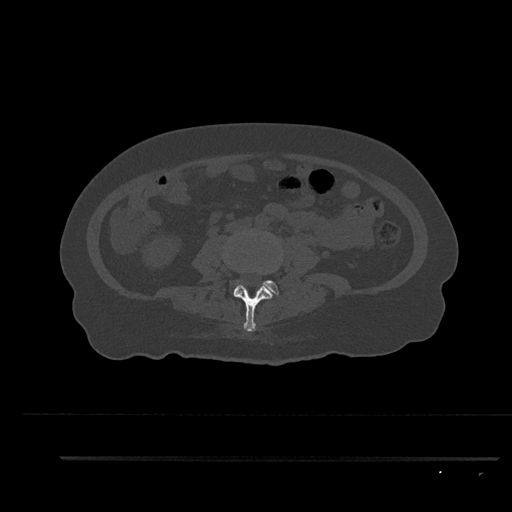
CT including the spine, one axial slice; slice 61 of 797 in the series (ordered by position); reconstruction kernel Br40s/3; 120 kVp; bone window (W 1800 / L 400 HU); 0.5 mm slice thickness; 512 × 512 image matrix, field of view 408 × 408 mm. Female patient, age 44 years. Case-level facts recorded for this patient, not image findings: primary cancer: renal; vertebrae with lytic lesions (as recorded): L1.
Annotated regions visible in this slice (semi-automatically segmented with operator editing):
- L3 vertebra: bounding box <228,263,276,331> (left, top, right, bottom; pixels)
- L4 vertebra: <235,280,280,295>